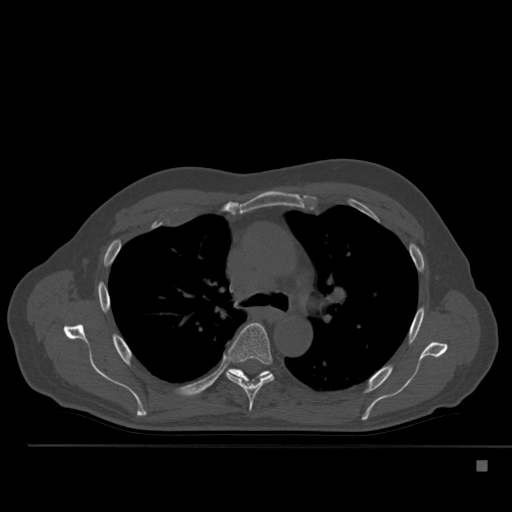
CT including the spine, one axial slice; slice 361 of 517 in the series (ordered by position); reconstruction kernel Br40s; 120 kVp; bone window (W 1800 / L 400 HU); 1.5 mm slice thickness; 512 × 512 image matrix, field of view 408 × 408 mm. Patient: male, 70 years. From the clinical record (not read from this slice): primary cancer: renal; vertebrae with lytic lesions (as recorded): T4, T6, T10, T12, L3, L4, L5.
Outlined on this slice (semi-automatically segmented with operator editing):
- T5 vertebra: bounding box (x1, y1, x2, y2) in pixels: (221, 323, 274, 412)
- T6 vertebra: (228, 369, 271, 381)